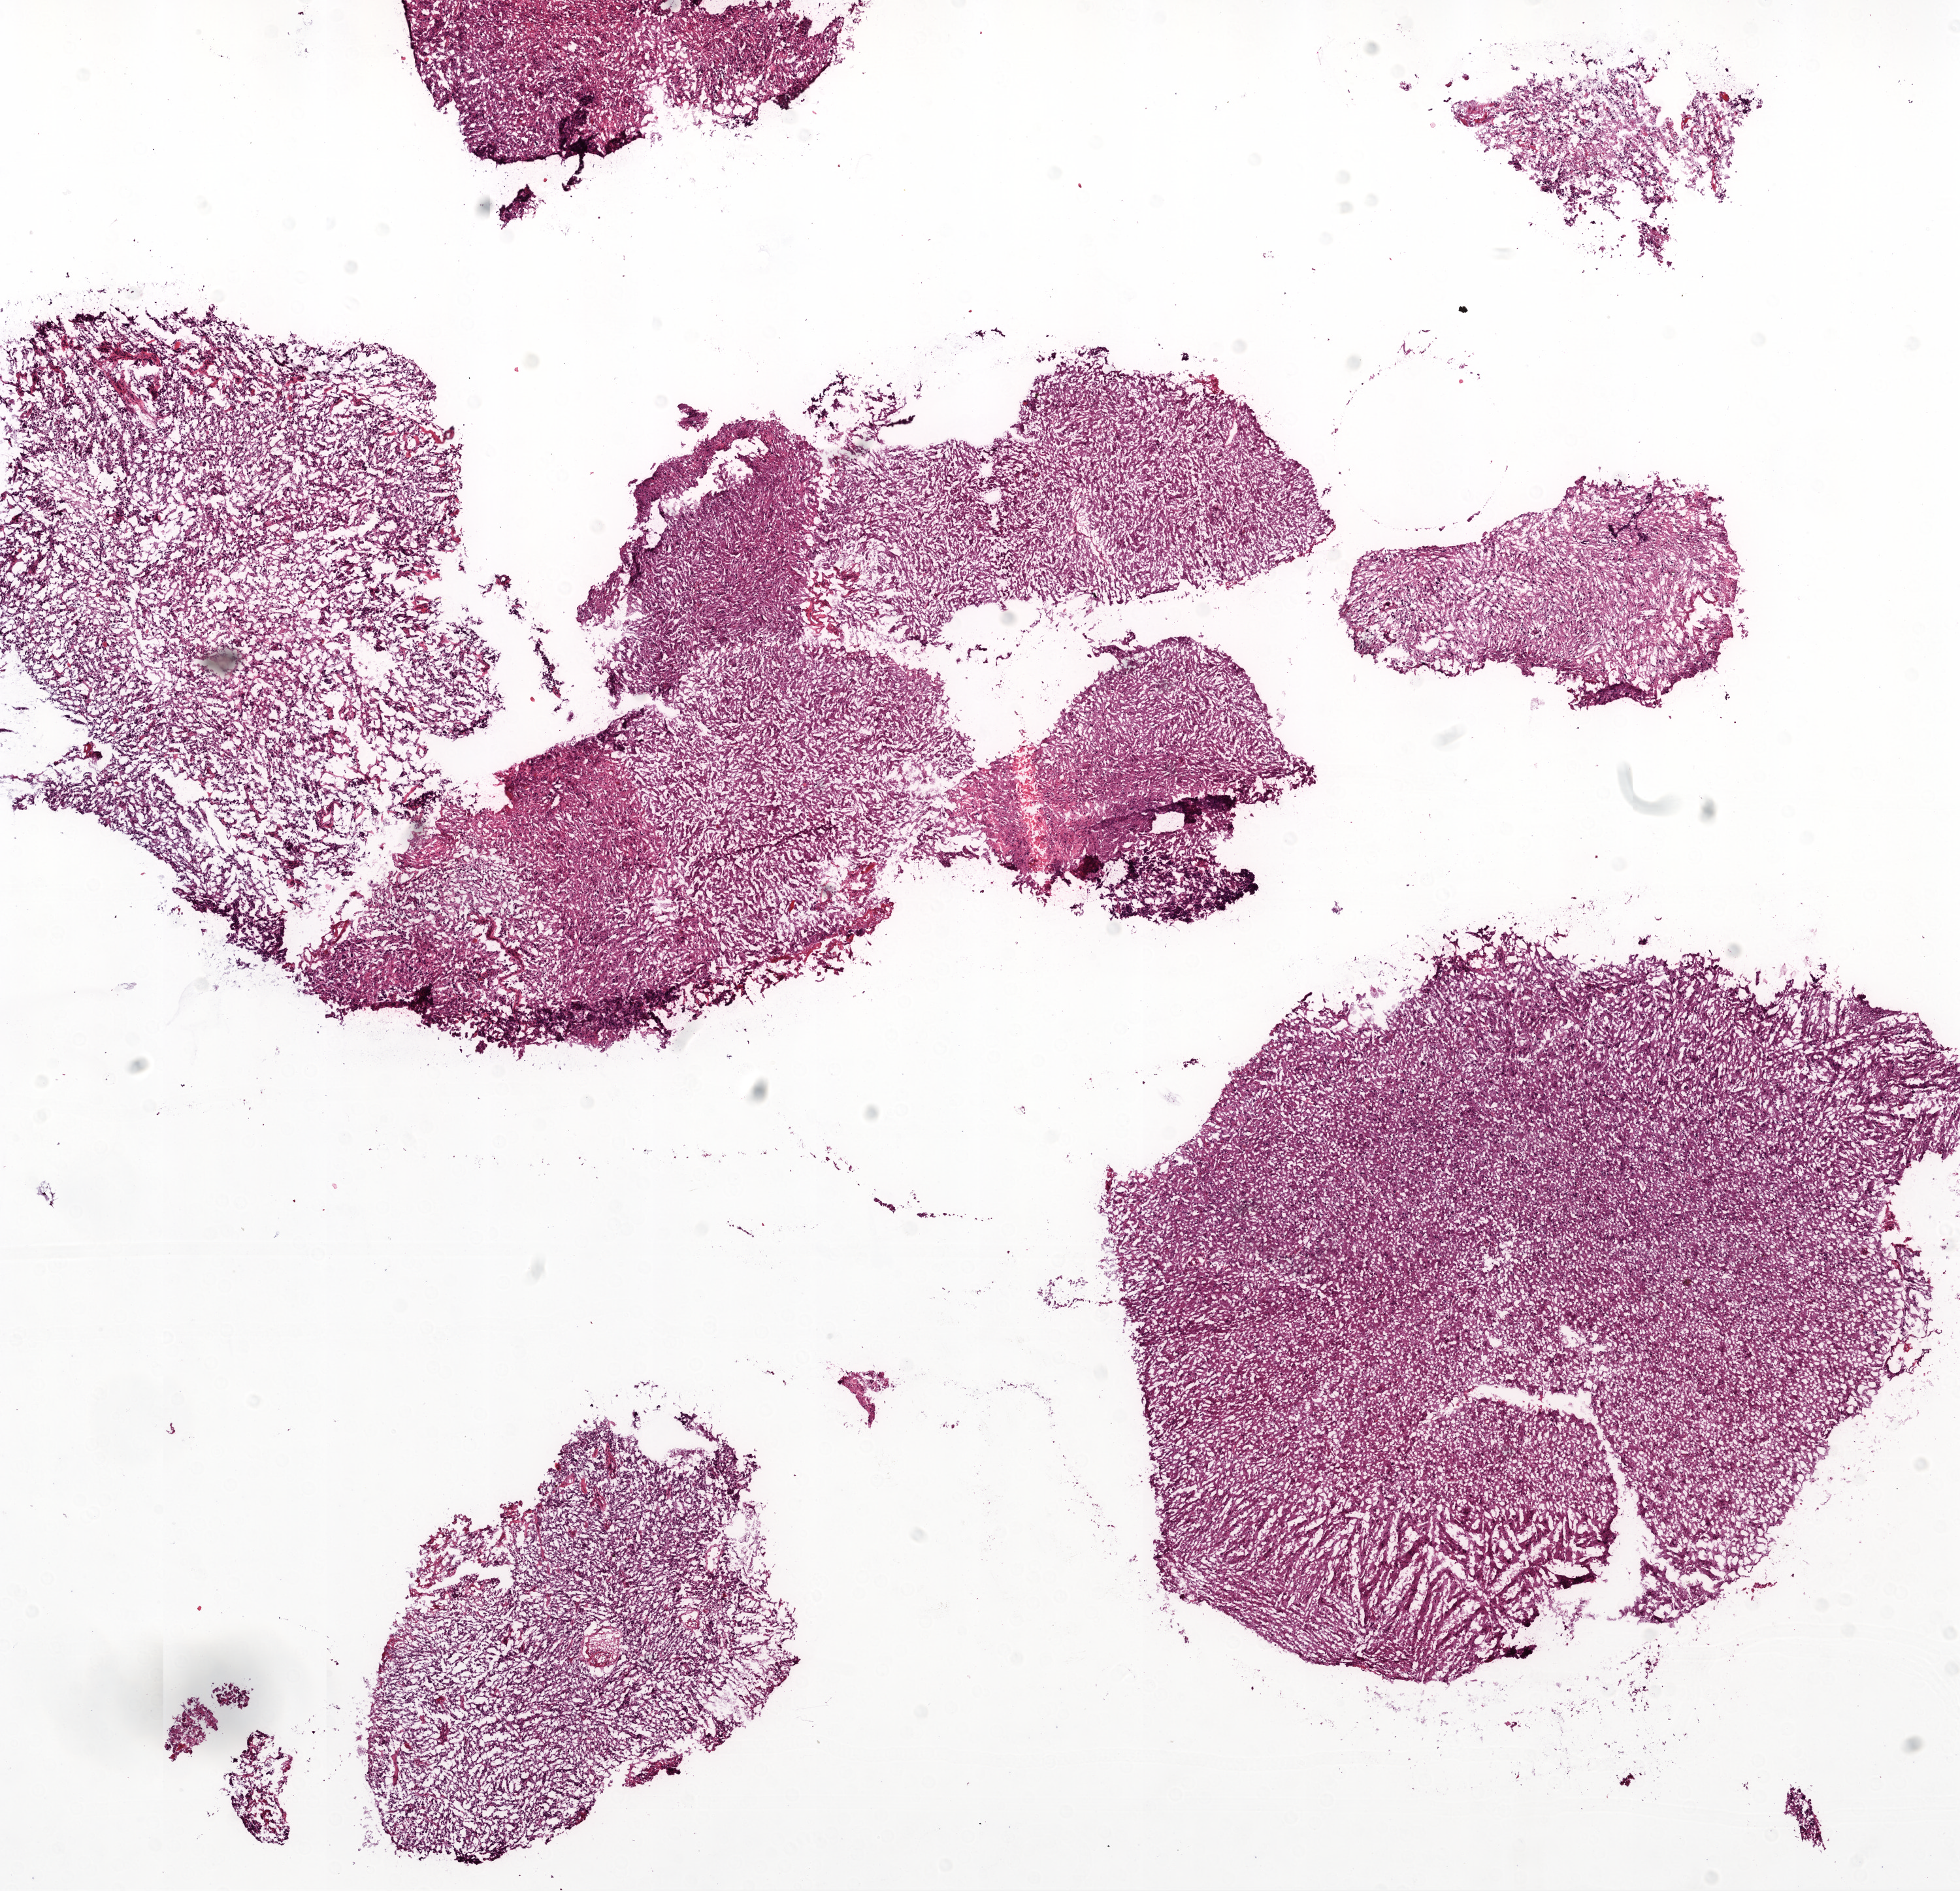
Digitized Hematoxylin and eosin (H&E) stained tissue section (whole slide) — whole scanned area (about 12.0 x 11.6 mm, slide scanned at 20x) shown as a low-resolution overview; frozen section; sample: primary tumour, brain. Male, age 65 years at initial diagnosis. Slide review estimates, as recorded: tumour cells 95%, tumour nuclei 95%.
Diagnosis: Glioblastoma.